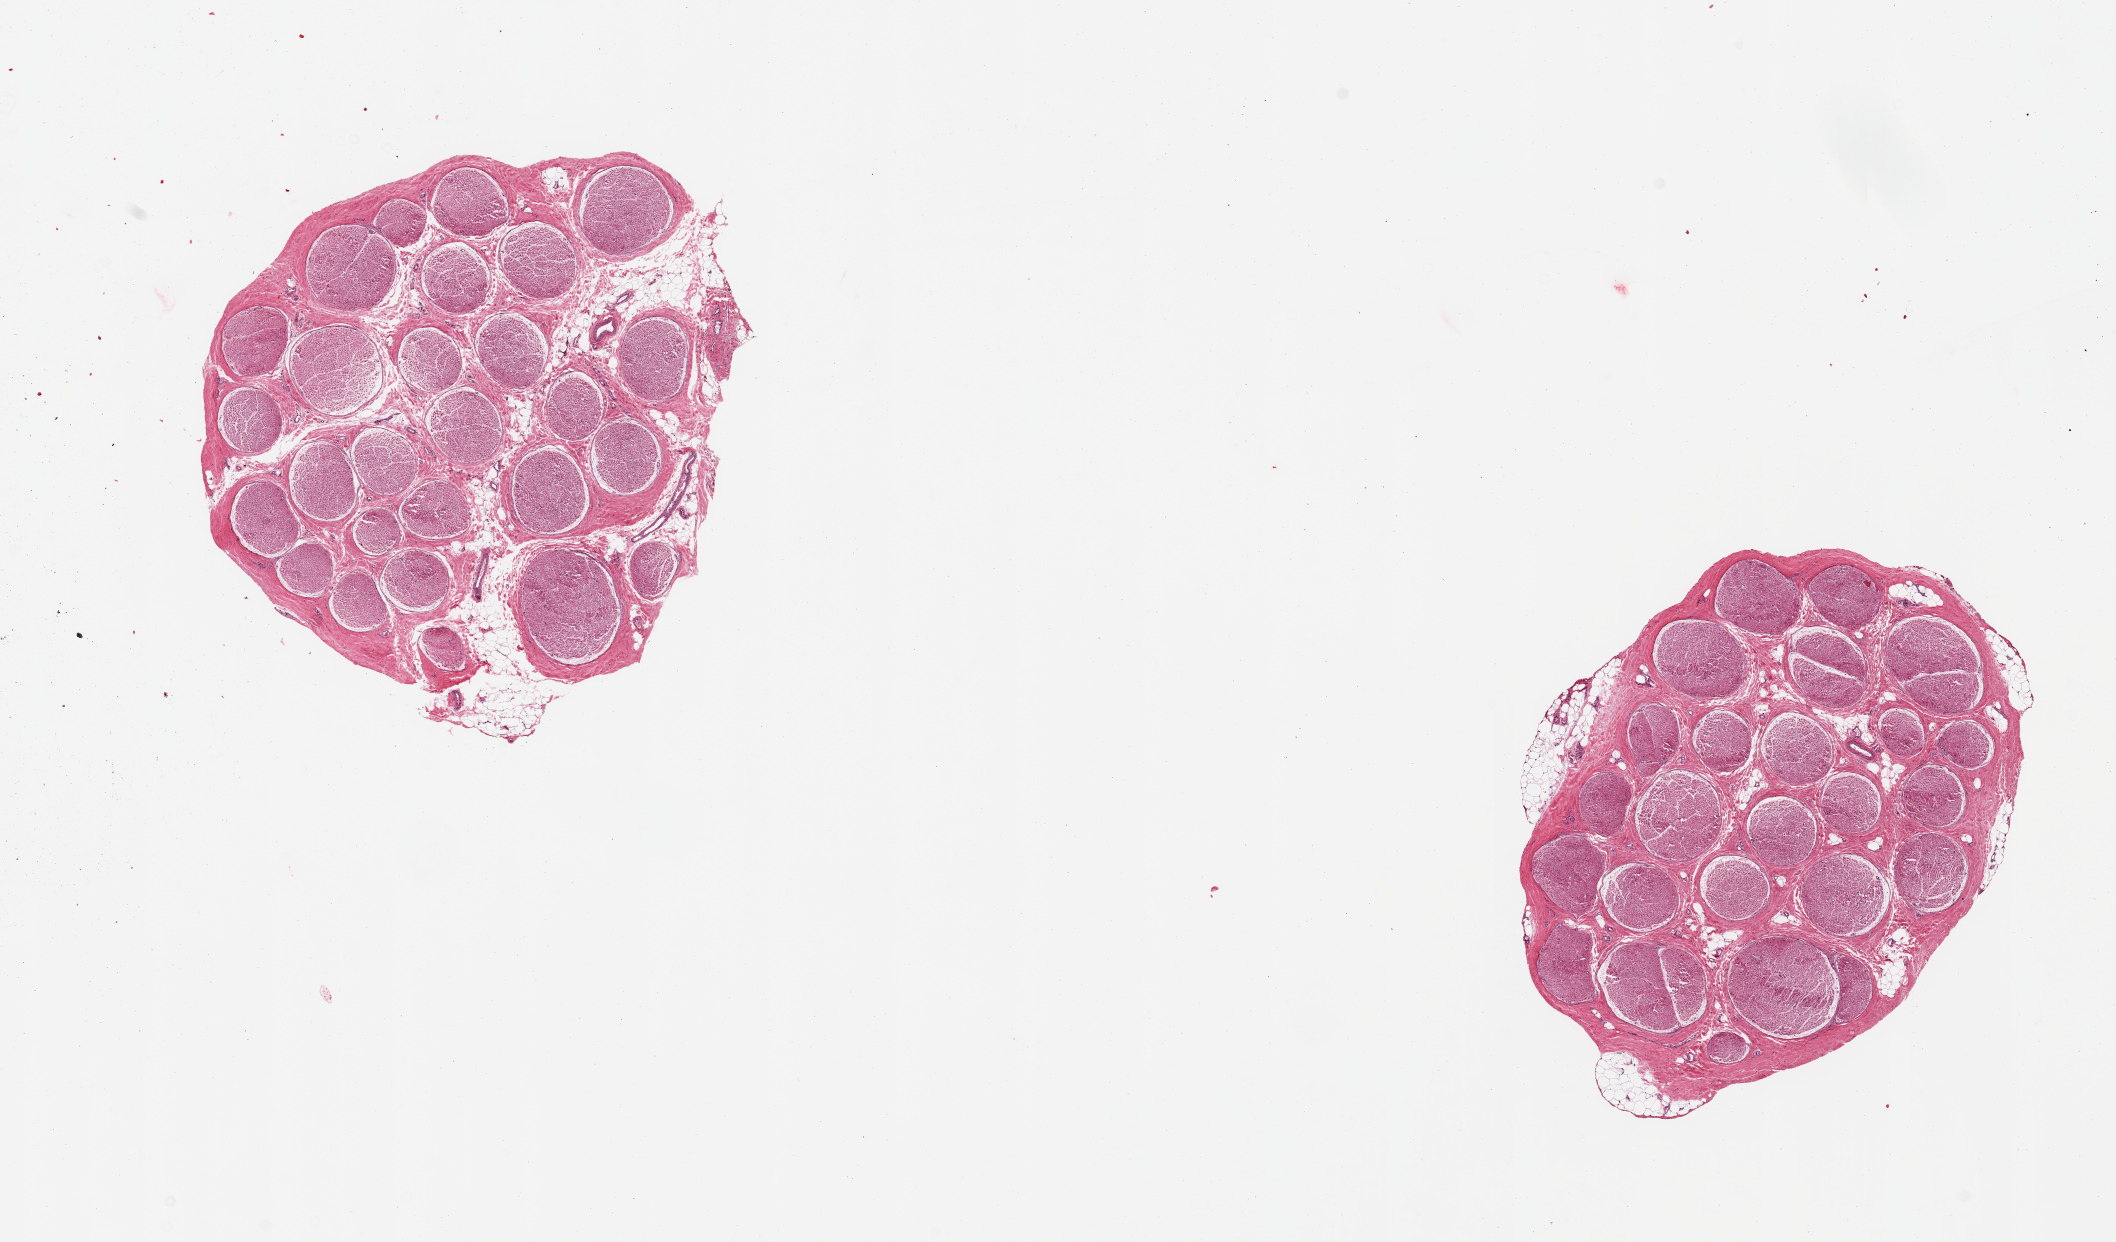
Hematoxylin and eosin (H&E) whole-slide image — whole scanned area (about 16.7 x 9.8 mm) shown as a low-resolution overview, PAXgene-fixed paraffin-embedded (PFPE) section, target tissue: tibial nerve, tissue donor sample. Female donor.
Review note (as recorded): 2 pieces; ~10% associated internal and external fat.